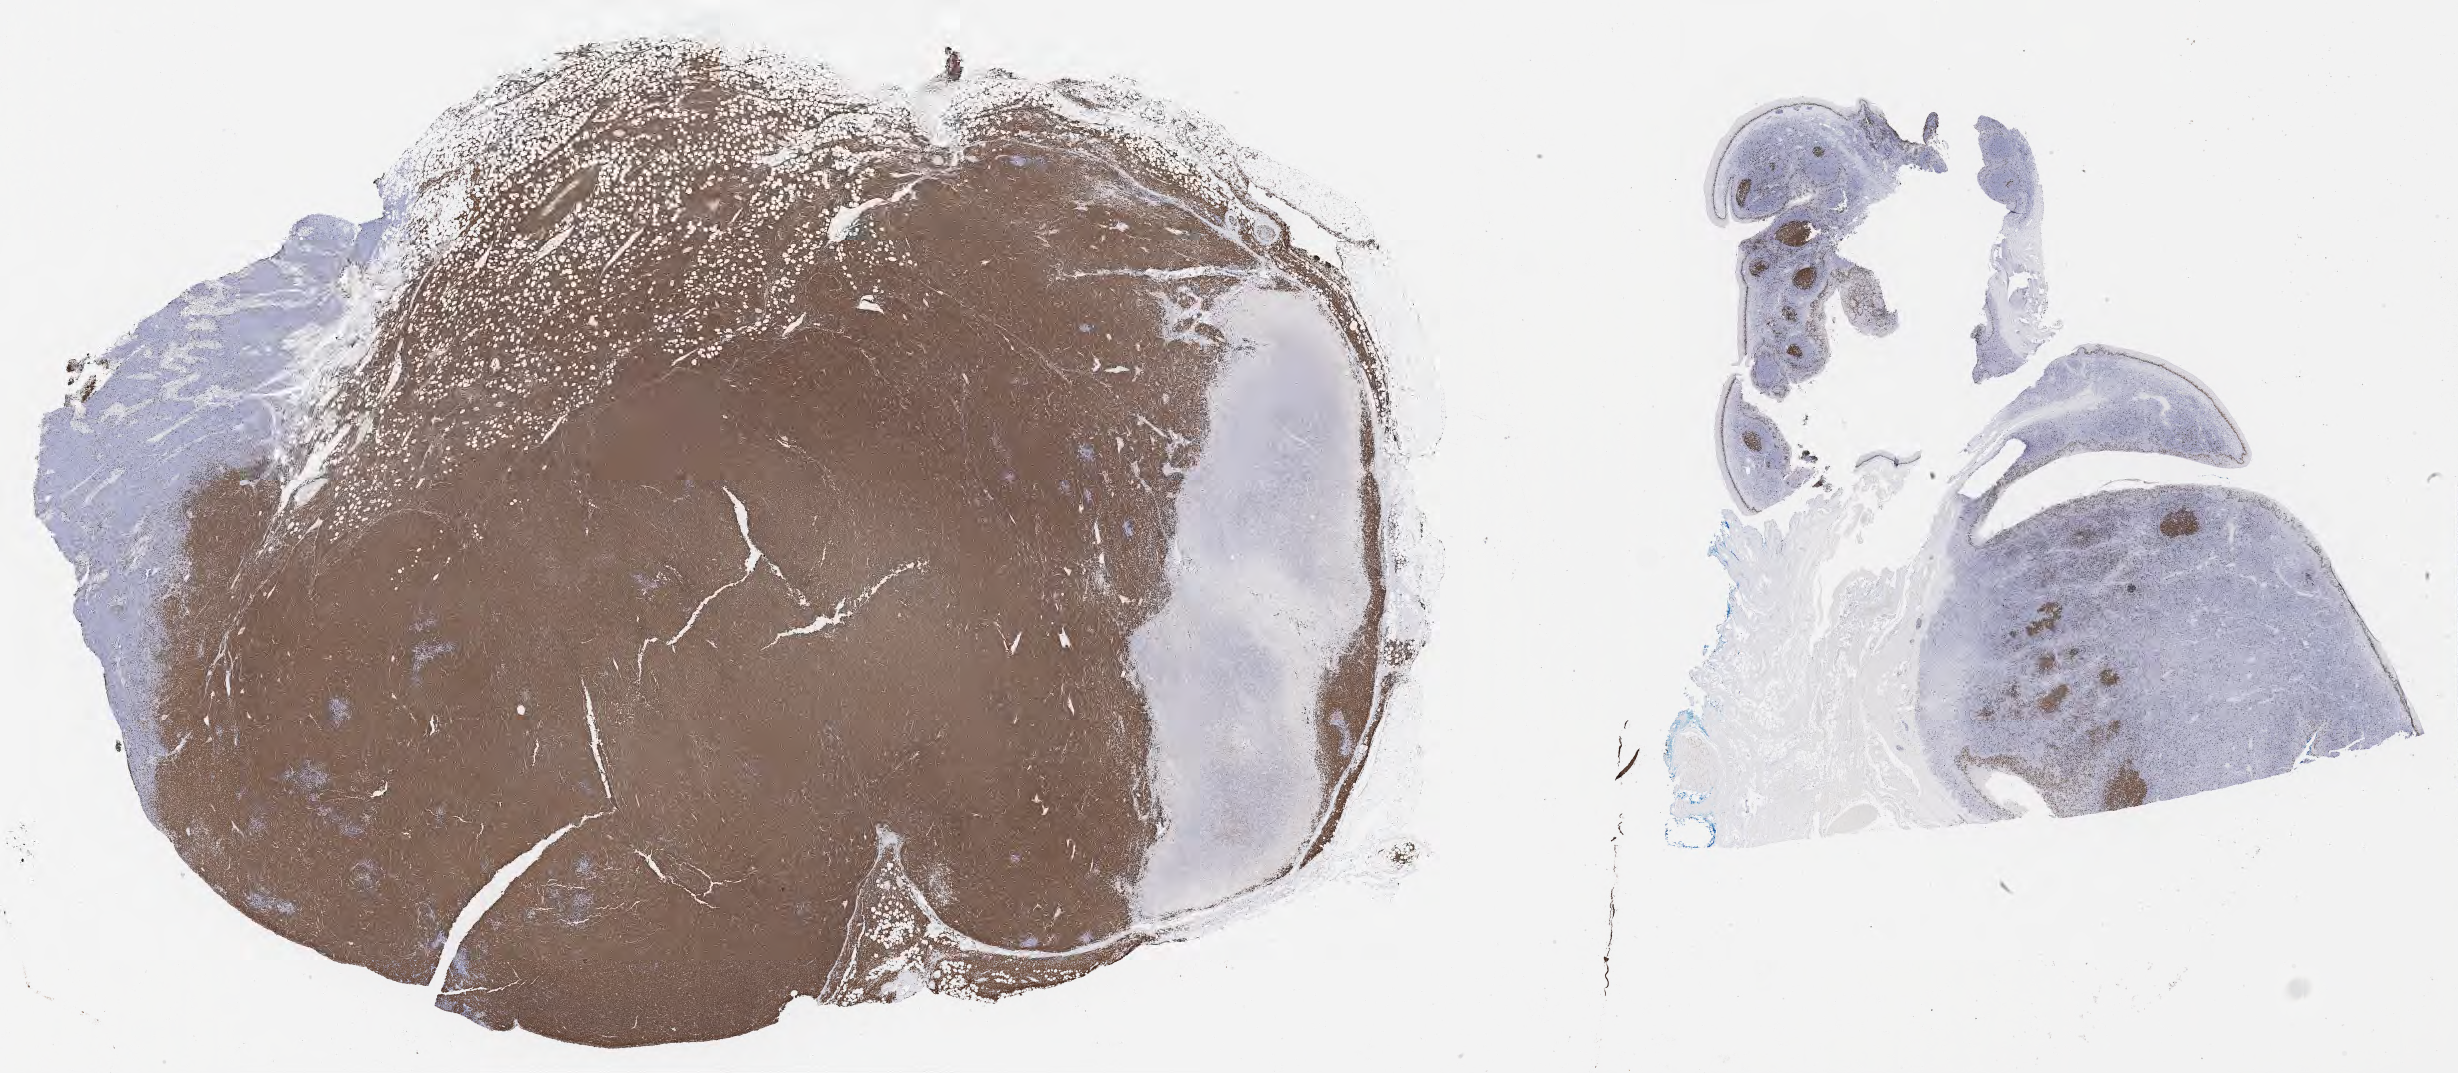
Immunohistochemistry (IHC) whole-slide image stained for Ki-67 — whole scanned area (about 39.8 x 17.4 mm) shown as a low-resolution overview; specimen: tumor tissue. Patient: male, 57 years old.
Histologic diagnosis: Burkitt lymphoma, NOS.